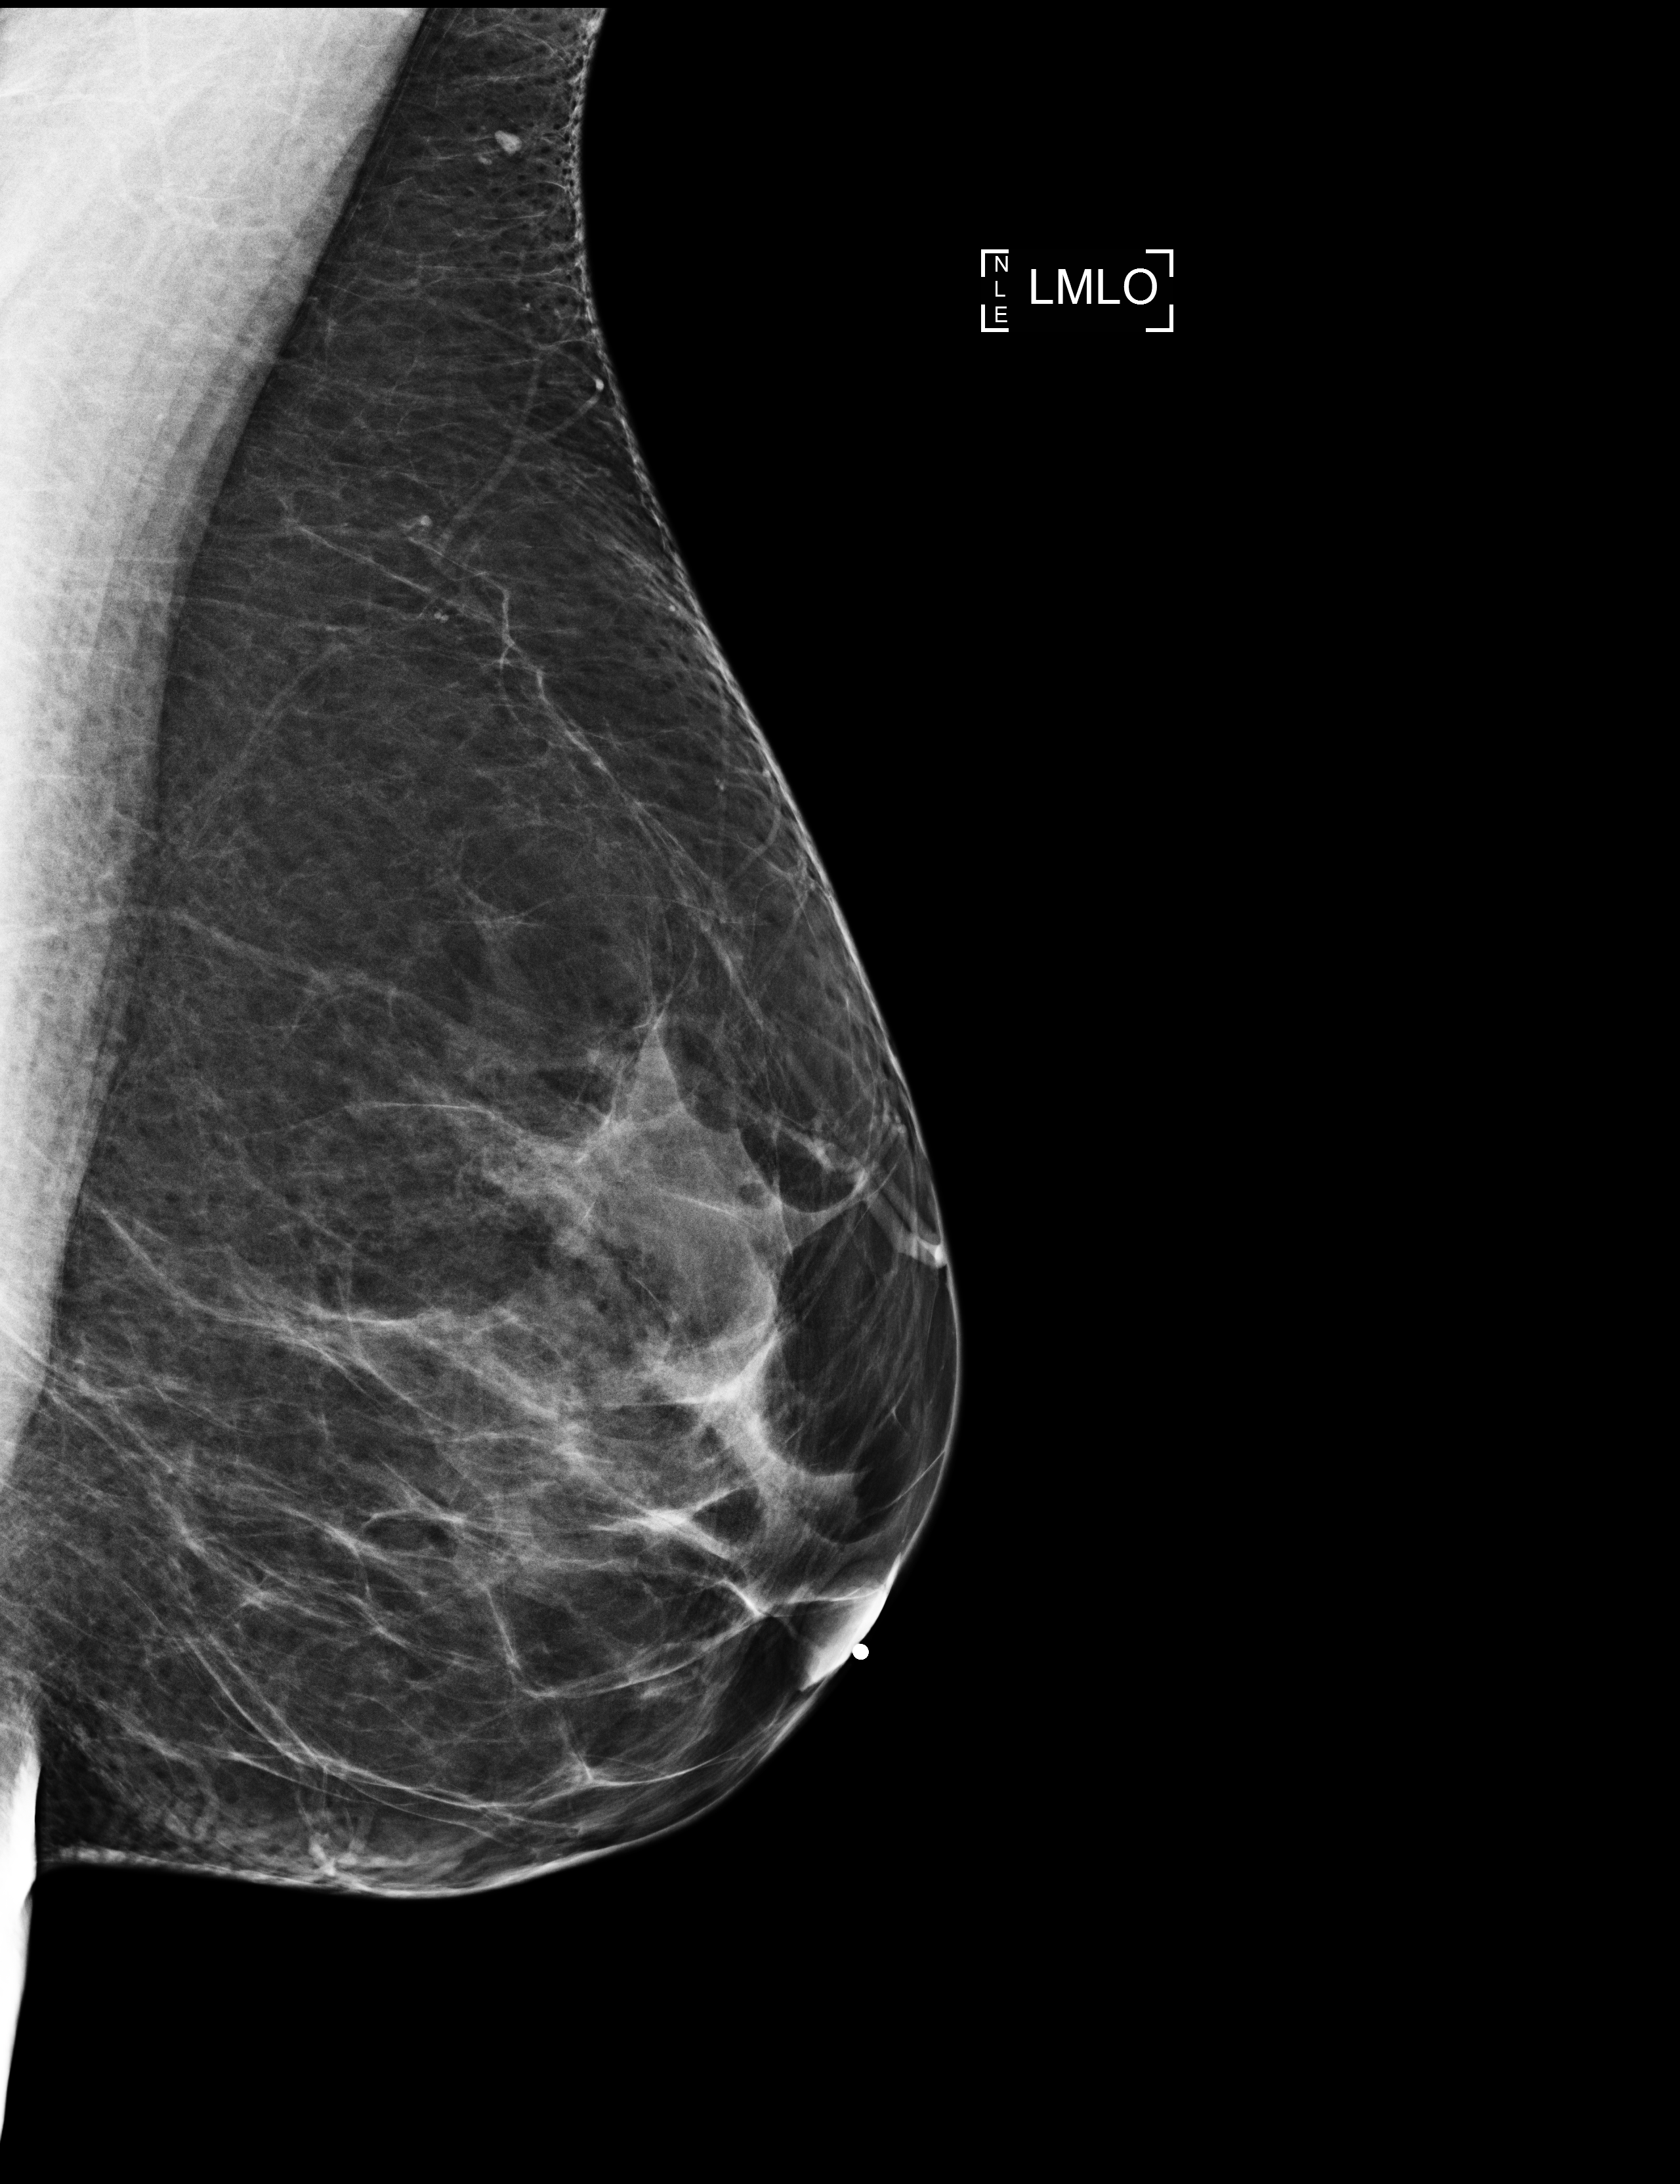
Screening examination; compressed breast thickness 71 mm.
Image type: full-field digital mammogram. Breast: left. Projection: mediolateral oblique (MLO) view.